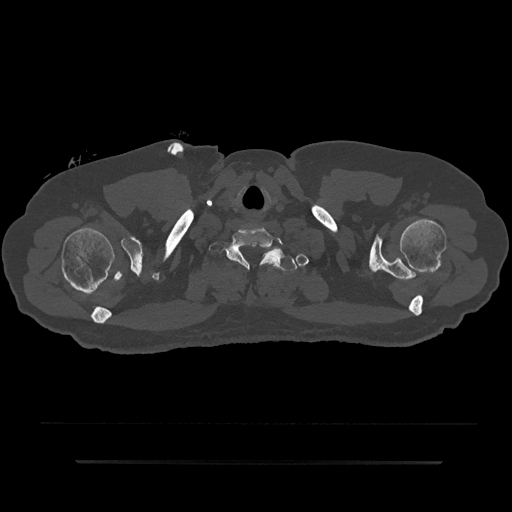
CT including the spine, one axial slice. Position 762 of 797 along the scan axis. Bone window (W 1800 / L 400 HU). 0.5 mm slice thickness. 512 × 512 image matrix. Male patient, age 59 years. From the clinical record (not read from this slice): primary cancer: bile ducts; vertebrae with lytic lesions (as recorded): T10.
Annotated regions visible in this slice (semi-automatic segmentation, software-assisted and operator-edited):
- T1 vertebra: box from (x=240, y=249) to (x=299, y=271) px